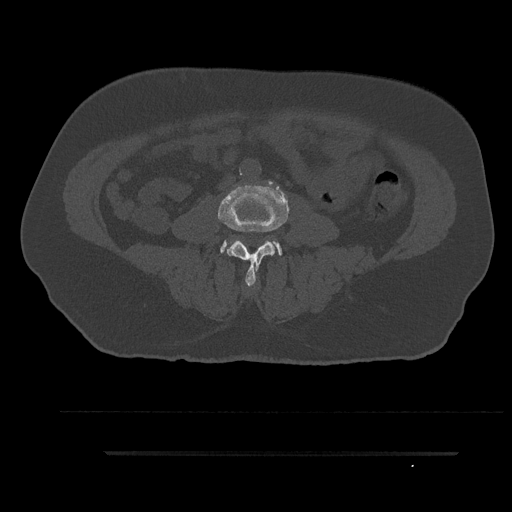
CT including the spine, one axial slice; slice 16 of 797 in the series (ordered by position); bone window (W 1800 / L 400 HU); 0.5 mm slice thickness; 512 × 512 image matrix, field of view 432 × 432 mm. Male patient, age 63 years. From the clinical record (not read from this slice): primary cancer: renal; vertebrae with lytic lesions (as recorded): T8.
Outlined on this slice (semi-automatic segmentation, software-assisted and operator-edited):
- L3 vertebra: bounding box [x1, y1, x2, y2] px = [218, 185, 289, 287]
- L4 vertebra: [220, 240, 282, 256]